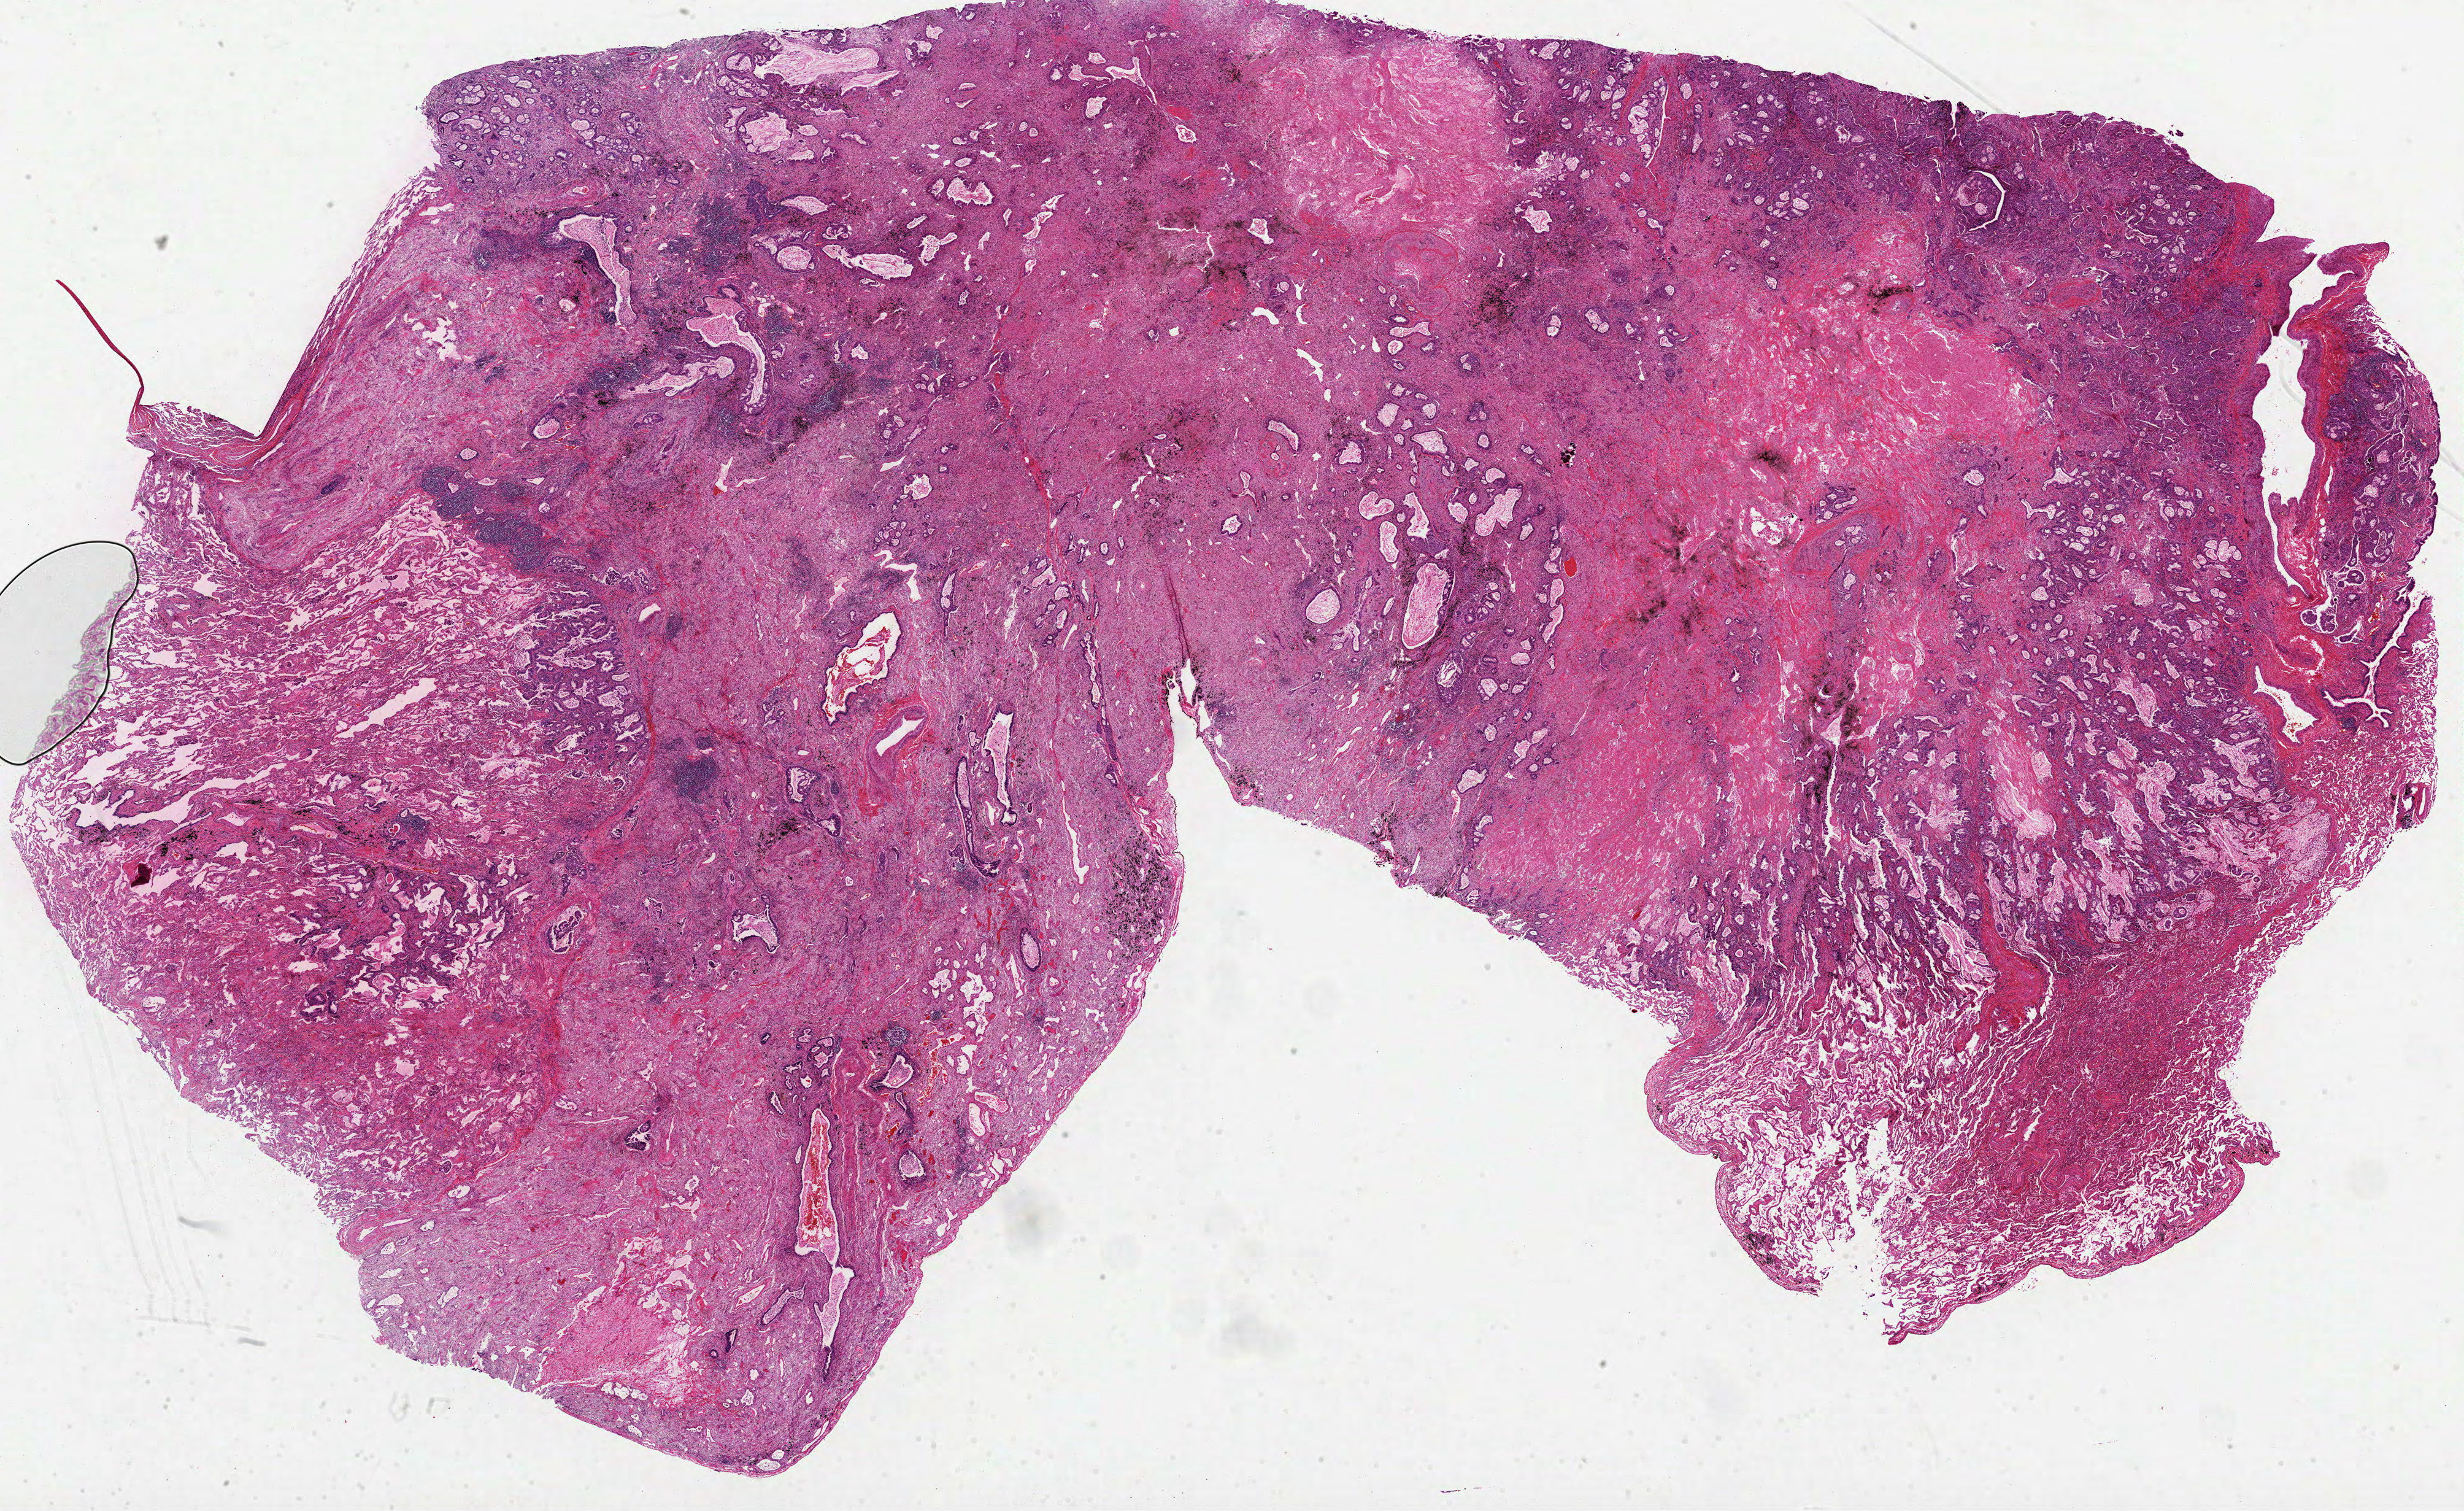
Whole-slide histology image, Hematoxylin and eosin (H&E) stained, a low-resolution overview of the entire scanned area, about 32.4 x 19.9 mm (acquisition: 40x scan). Formalin-fixed paraffin-embedded (FFPE) diagnostic section. Primary tumour sample from the lung. Patient: male, age at initial diagnosis 77 years.
Pathologic diagnosis: Adenocarcinoma, NOS (upper lobe, lung). TNM: T3 N2 M0. AJCC pathologic stage: IIIA.